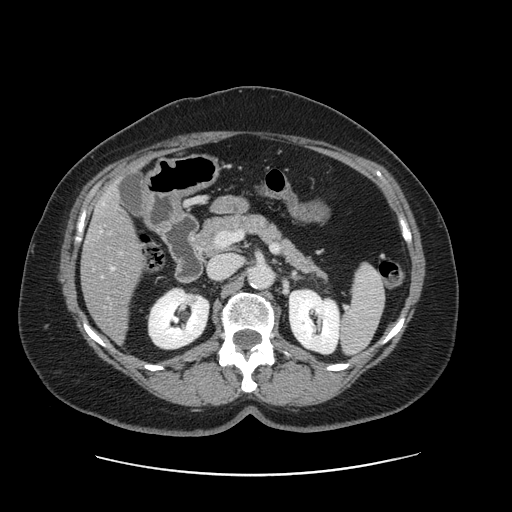
Contrast-enhanced abdominal CT, one axial slice; slice 68 of 161 in the series (ordered by position); 120 kVp; intravenous contrast given; soft-tissue window (W 400 / L 40 HU); 512 × 512 image matrix, field of view 398 × 398 mm. Female patient, age 62 years. Case-level facts recorded for this patient, not image findings: diagnosis: colorectal cancer liver metastases, imaged before liver resection; multiple liver metastases: no; largest metastasis: 2.5 cm; chemotherapy before resection: yes.
Structures marked on this image (manually delineated by an expert):
- liver: bounding box <82,188,142,340> (left, top, right, bottom; pixels)
- portal vein (with intrahepatic branches): <111,268,114,270>